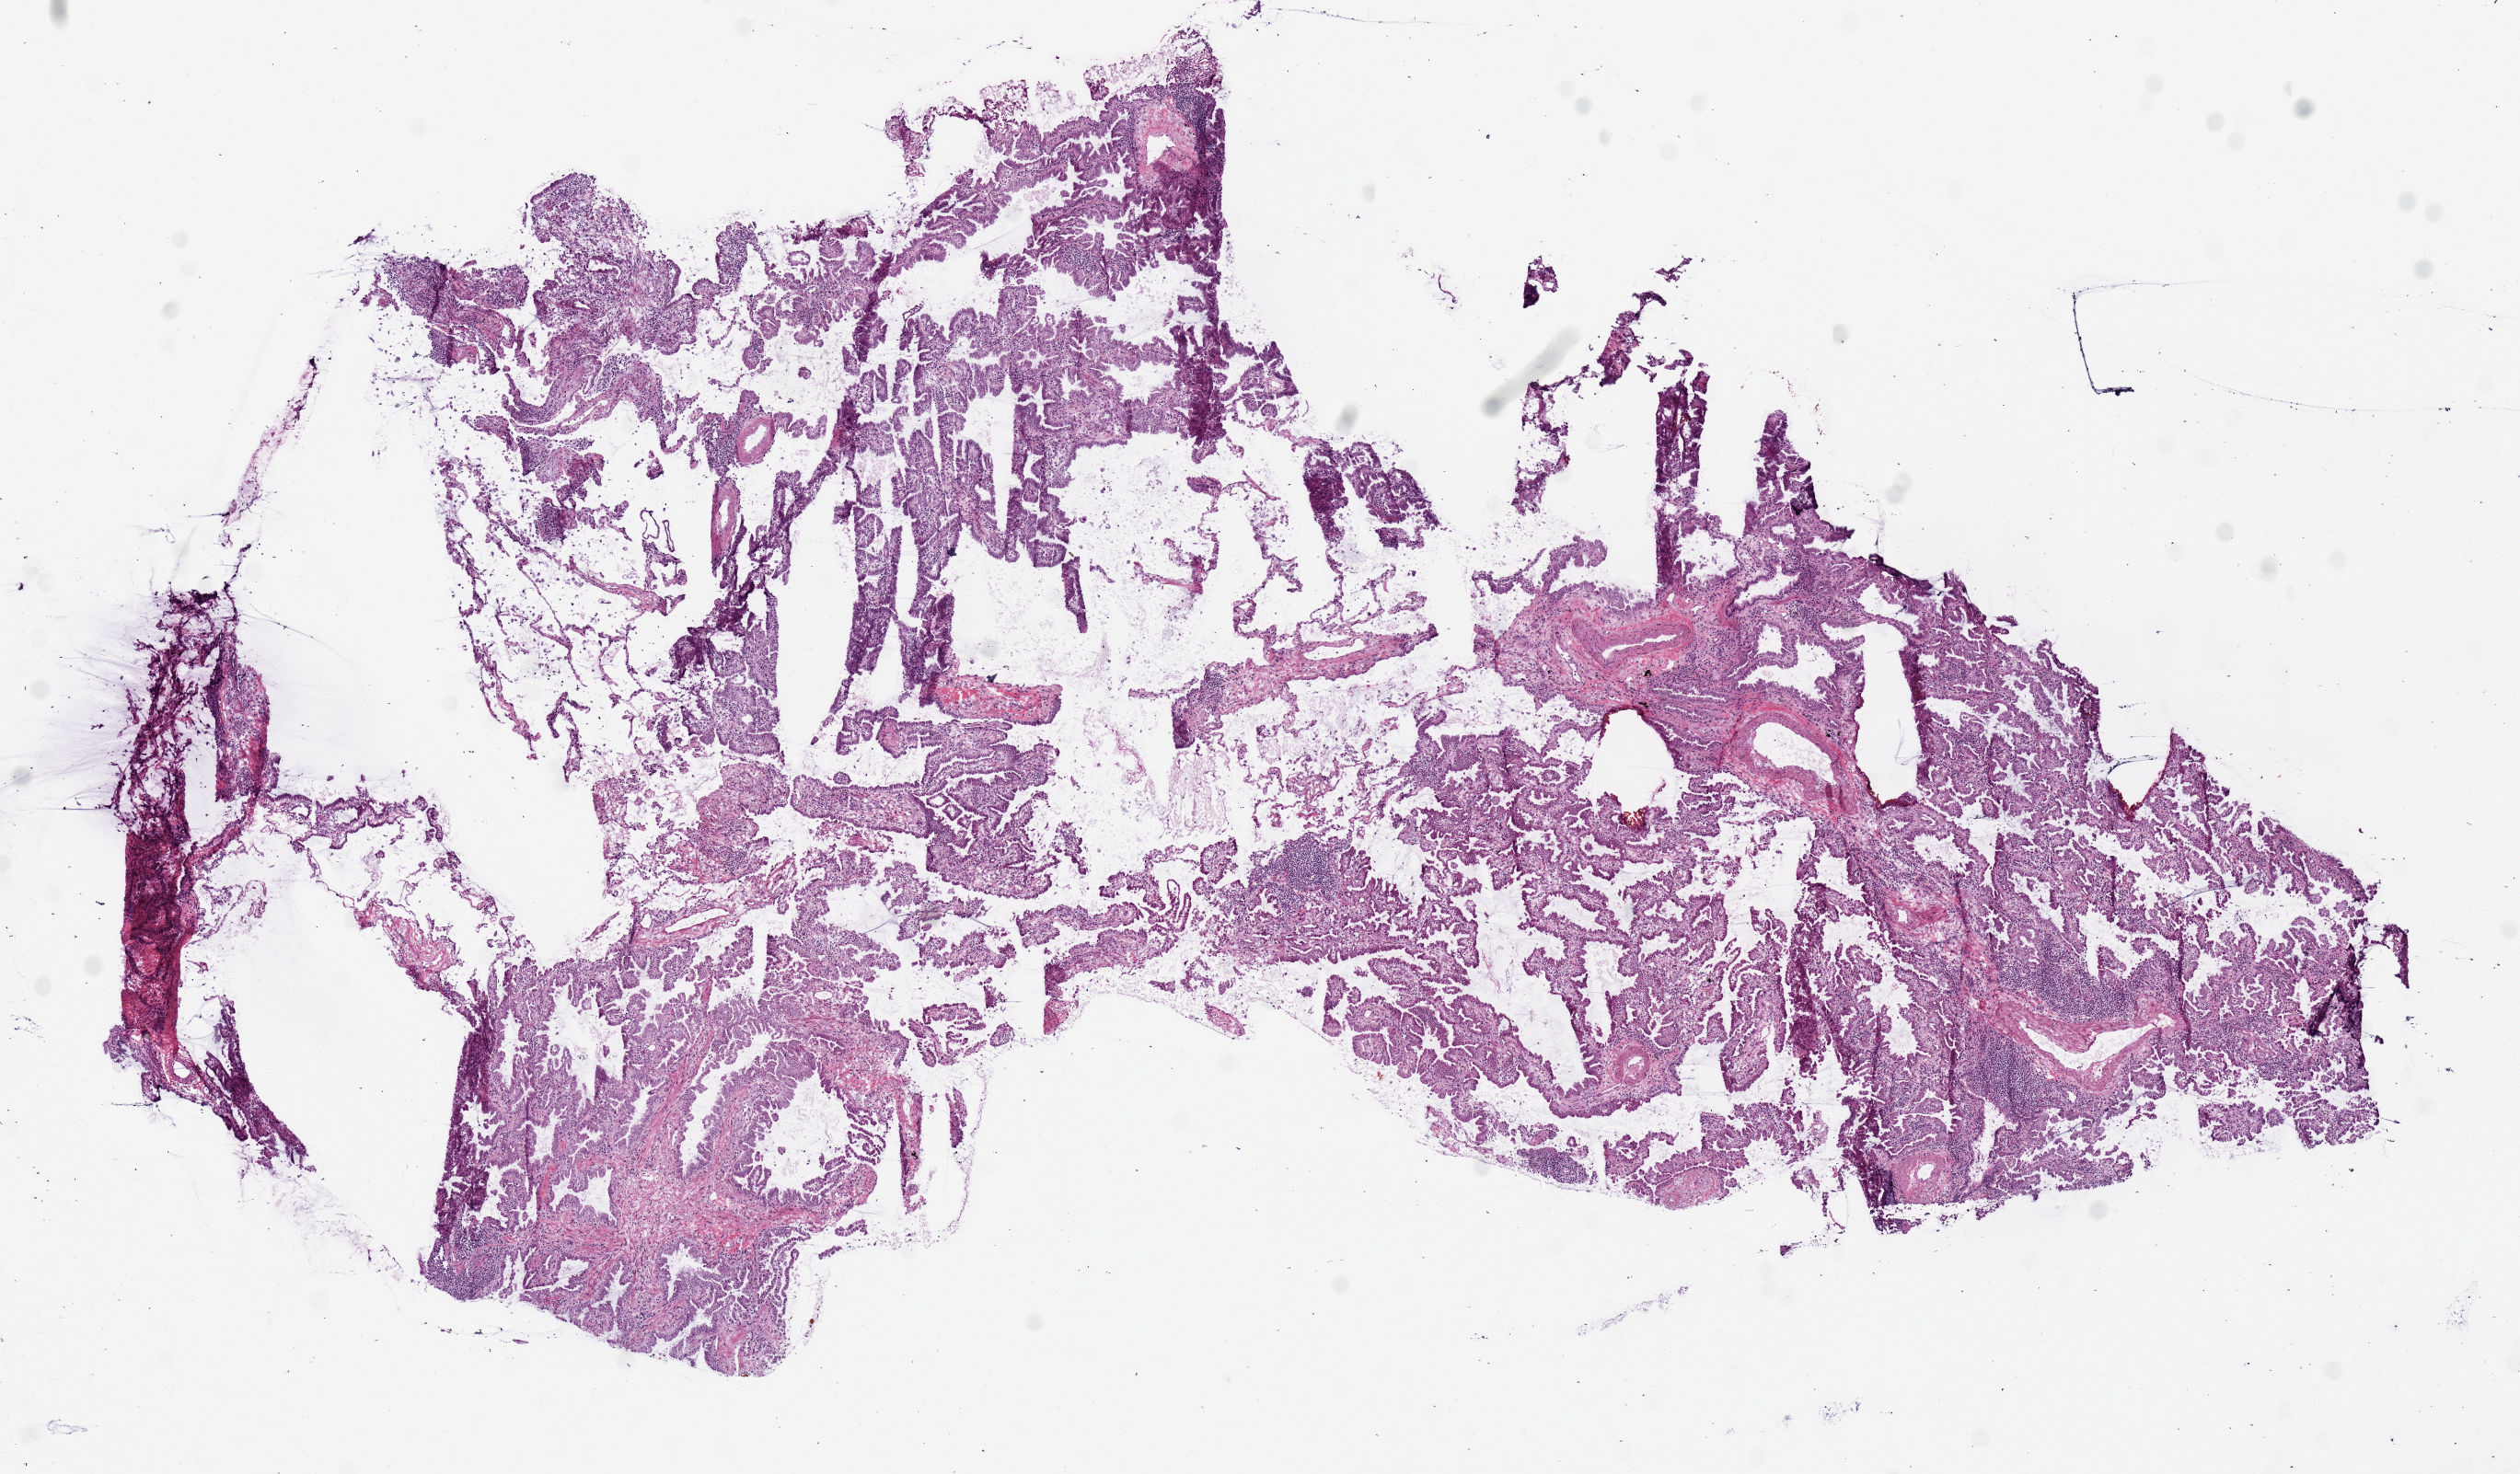
Whole-slide histology image, Hematoxylin and eosin (H&E) stained — whole scanned area (about 10.8 x 6.3 mm, slide scanned at 20x) shown as a low-resolution overview; frozen section from the top of the tissue portion; primary tumour sample from the lung. Patient: male, age at initial diagnosis 85 years. Slide review estimates, as recorded: tumour cells 75%, tumour nuclei 65%, normal cells 0%, stromal cells 25%, necrosis 0%.
Diagnosis: Adenocarcinoma with mixed subtypes.